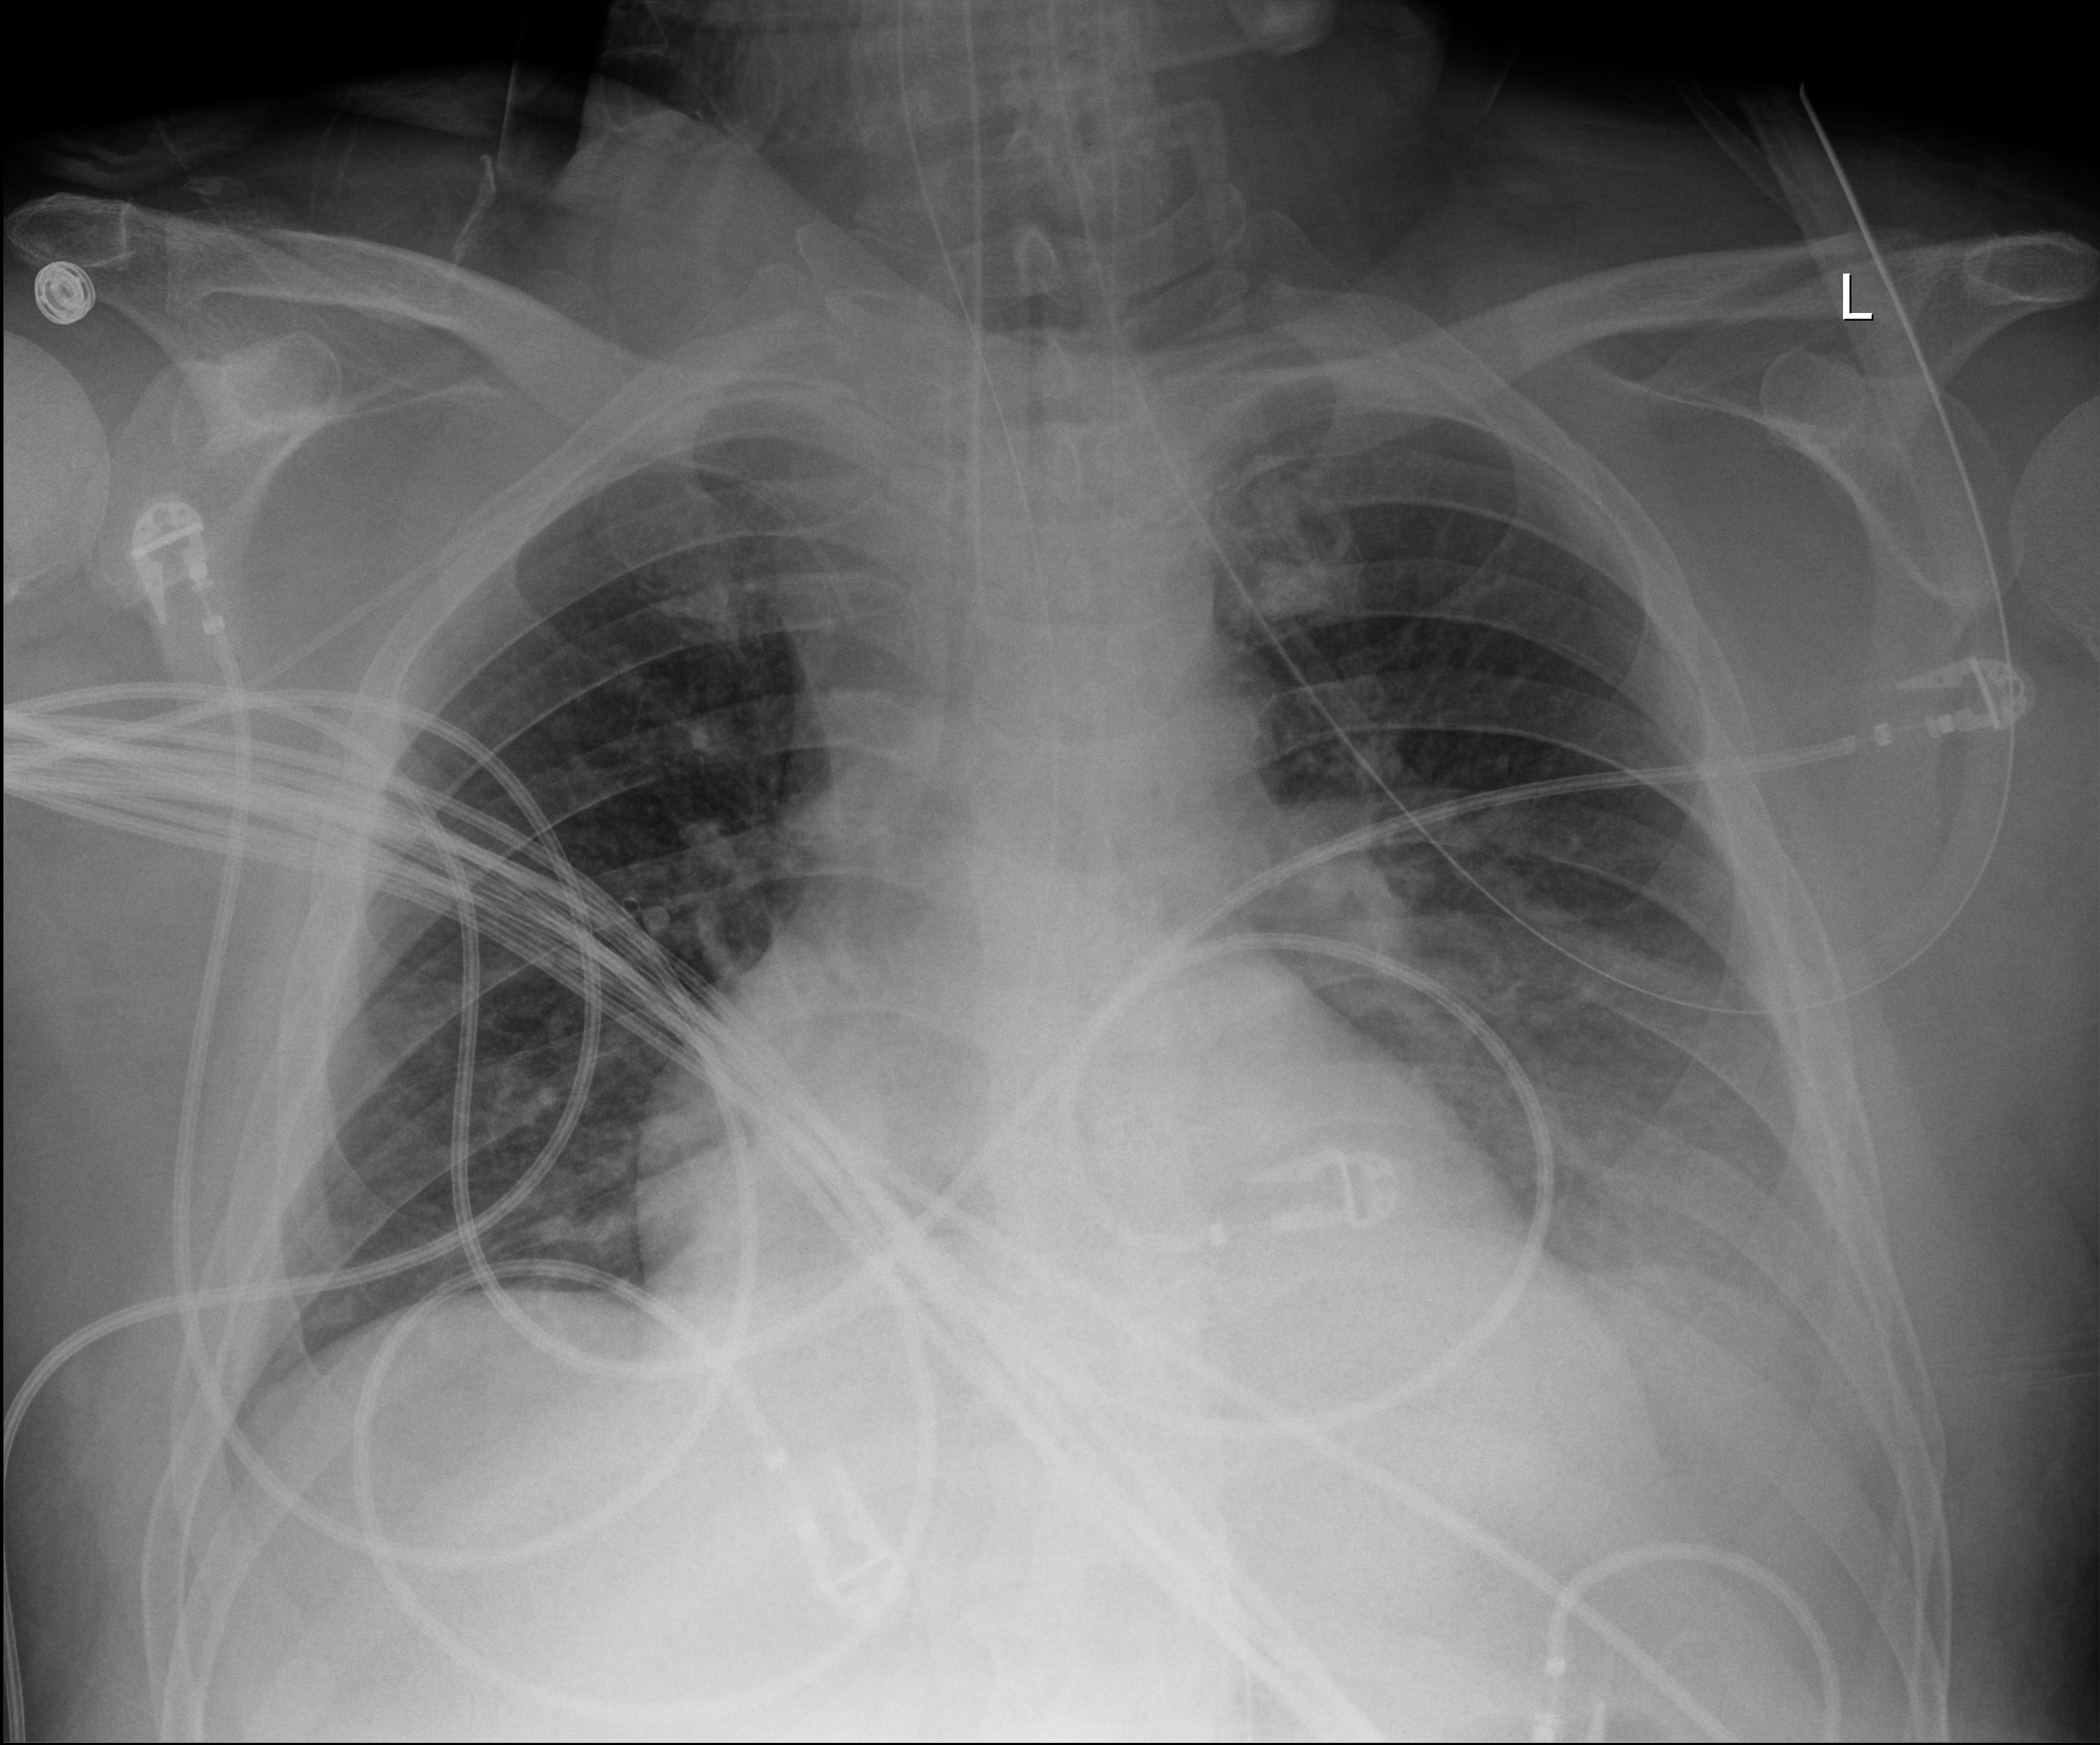
Chest X-ray (portable). Male patient hospitalised with COVID-19, age 18–59 years.
Hospital-stay facts (about this admission, not read from this image; timing relative to this image not recorded): mechanically ventilated during this hospital stay: yes.